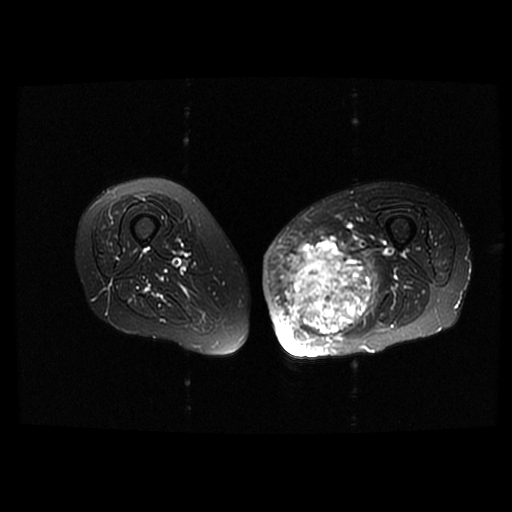
MRI of an extremity soft-tissue mass, one axial slice; position 33 of 42 along the scan axis; T2-weighted fat-saturated; 6 mm slice thickness; 512 × 512 image matrix, field of view 420 × 420 mm. Female patient. Case-level facts recorded for this patient, not image findings: histological type: pleomorphic leiomyosarcoma; grade: high; site of the primary tumour: left thigh.
Outlined on this slice (outlined manually by an expert reader):
- gross tumour volume including surrounding oedema: bounding box [x1, y1, x2, y2] px = [279, 237, 380, 338]
- gross tumour volume (mass): [279, 240, 371, 337]